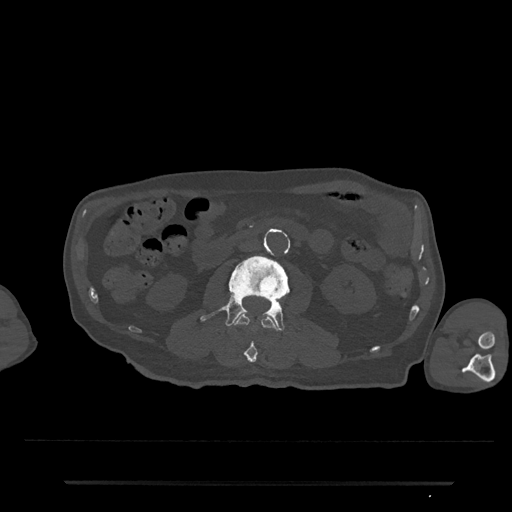
CT including the spine, one axial slice. Position 14 of 797 along the scan axis. Bone window (W 1800 / L 400 HU). 0.5 mm slice thickness. 512 × 512 image matrix, field of view 427 × 427 mm. Patient: male, 74 years. From the clinical record (not read from this slice): primary cancer: prostate.
Outlined on this slice (semi-automatic segmentation, software-assisted and operator-edited):
- L2 vertebra: bounding box (x1, y1, x2, y2) in pixels: (234, 314, 279, 363)
- L3 vertebra: (200, 256, 290, 331)